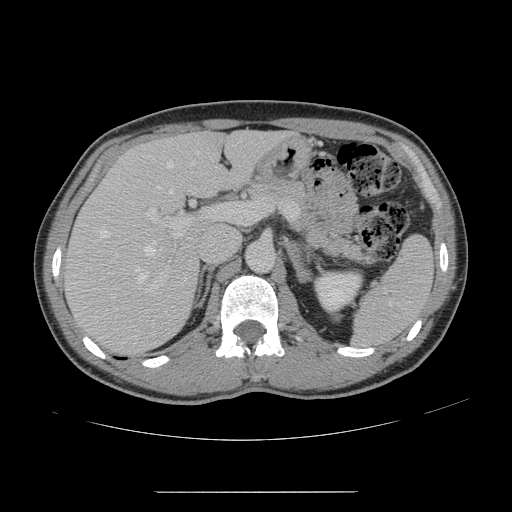
Contrast-enhanced abdominal CT, one axial slice. Slice 90 of 178 in the series (ordered by position). Intravenous contrast given. Soft-tissue window (W 400 / L 40 HU). 512 × 512 image matrix. Male patient, age 53 years. Case-level facts recorded for this patient, not image findings: diagnosis: colorectal cancer liver metastases, imaged before liver resection; multiple liver metastases: yes; largest metastasis: 2.4 cm; disease in both lobes: no.
Structures marked on this image (outlined manually by an expert reader):
- hepatic veins: bounding box [x1, y1, x2, y2] px = [100, 151, 199, 285]
- liver: [67, 131, 282, 353]
- planned liver remnant (the part of the liver to remain after resection): [150, 131, 282, 194]
- portal vein (with intrahepatic branches): [146, 198, 267, 289]